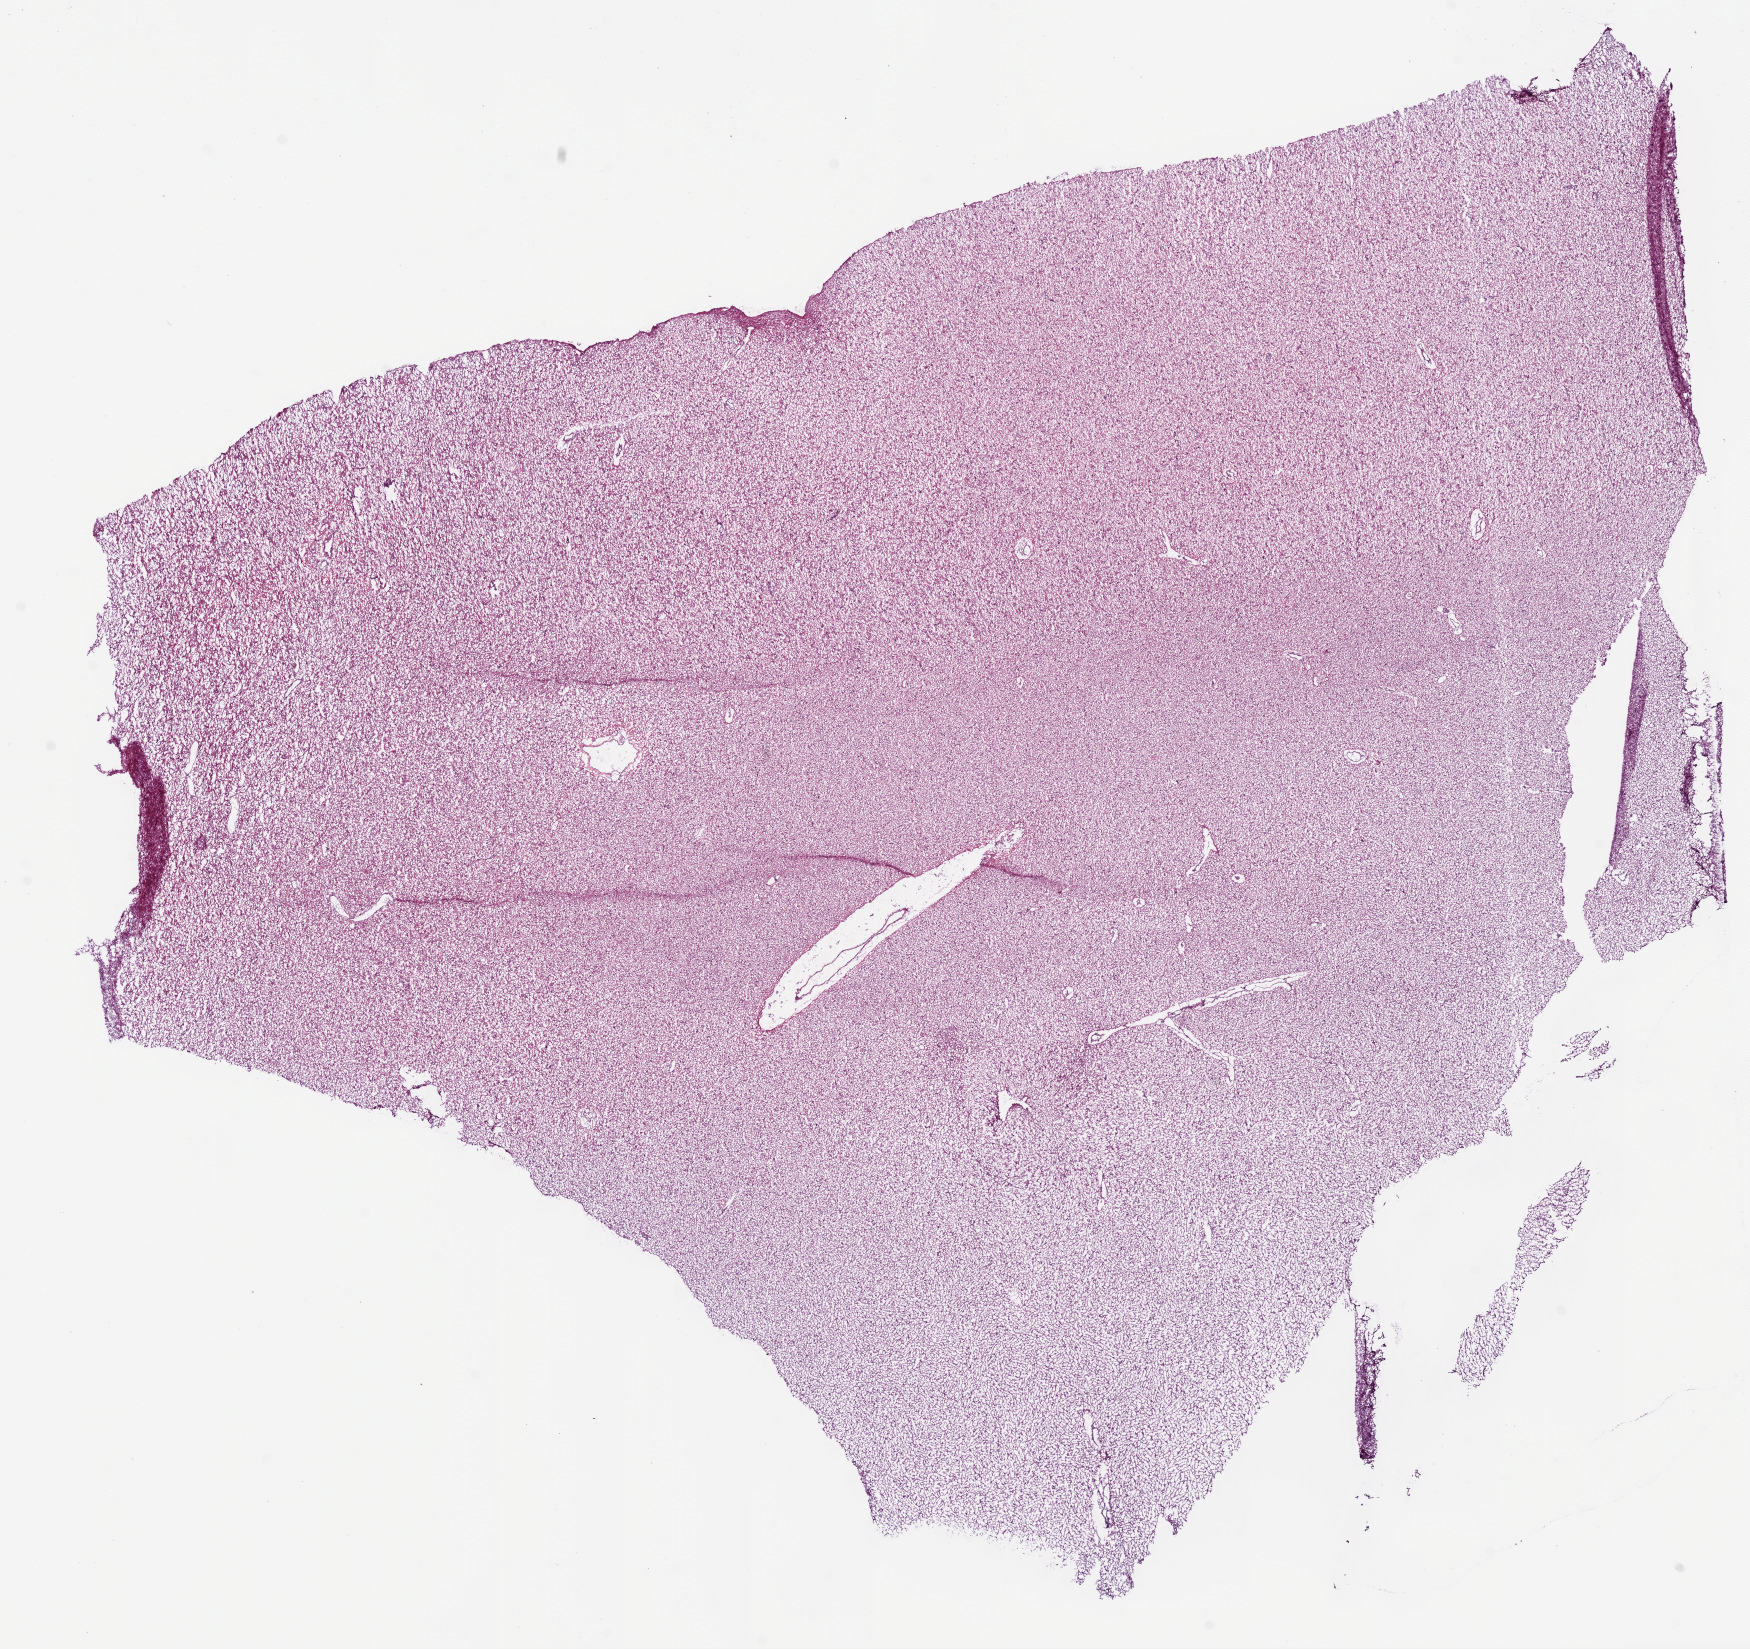
Digitized H&E tissue section (whole slide) — whole scanned area (about 14.0 x 13.2 mm, from a 20x scan) shown as a low-resolution overview. Frozen section from the bottom of the tissue portion. Sample: primary tumour, brain. Male, age 33 years at initial diagnosis. Histologic grade: G3 (poorly differentiated). Slide review estimates, as recorded: tumour cells 100%, tumour nuclei 60%, normal cells 0%, stromal cells 0%, necrosis 0%.
* histologic diagnosis: Astrocytoma, anaplastic (cerebrum)
* laterality: right